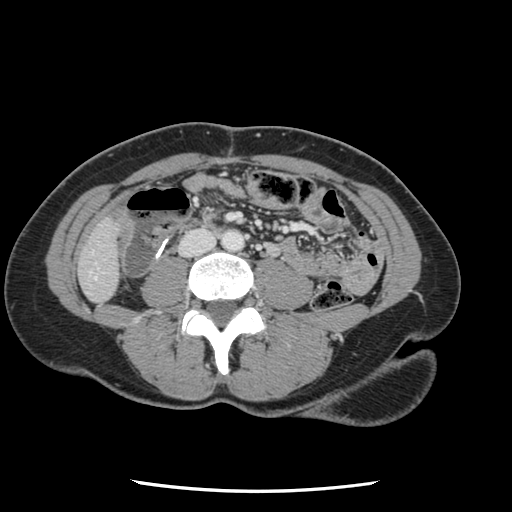
Contrast-enhanced abdominal CT, one axial slice; slice 7 of 134 in the series (ordered by position); 120 kVp; intravenous contrast given; soft-tissue window (W 400 / L 40 HU); 2.5 mm slice thickness; 512 × 512 image matrix. Female patient, age 43 years. From the clinical record (not read from this slice): diagnosis: colorectal cancer liver metastases, imaged before liver resection; multiple liver metastases: yes; largest metastasis: 3.4 cm; disease in both lobes: yes.
Annotated regions visible in this slice (expert manual segmentation):
- liver: box from (x=80, y=221) to (x=119, y=302) px
- planned liver remnant (the part of the liver to remain after resection): (x=80, y=221)–(x=119, y=302)